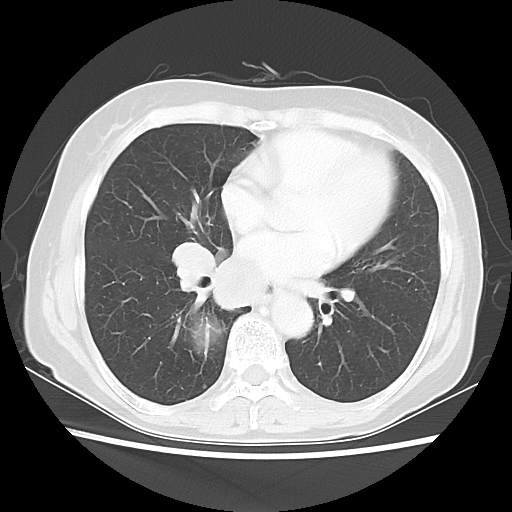
Chest CT, one axial slice. Position 24 of 56 along the scan axis. 120 kVp. Lung window (W 1500 / L -600 HU). 5 mm slice thickness. 512 × 512 image matrix, field of view 332 × 332 mm. Patient: female, 66 years. Case-level facts recorded for this patient, not image findings: clinical TNM (as recorded): T2 N3 M0; histopathological grade: G3.
Structures marked on this image (bounding box drawn by a radiologist):
- lung tumour (recorded histology: small cell carcinoma): box from (x=185, y=305) to (x=219, y=354) px